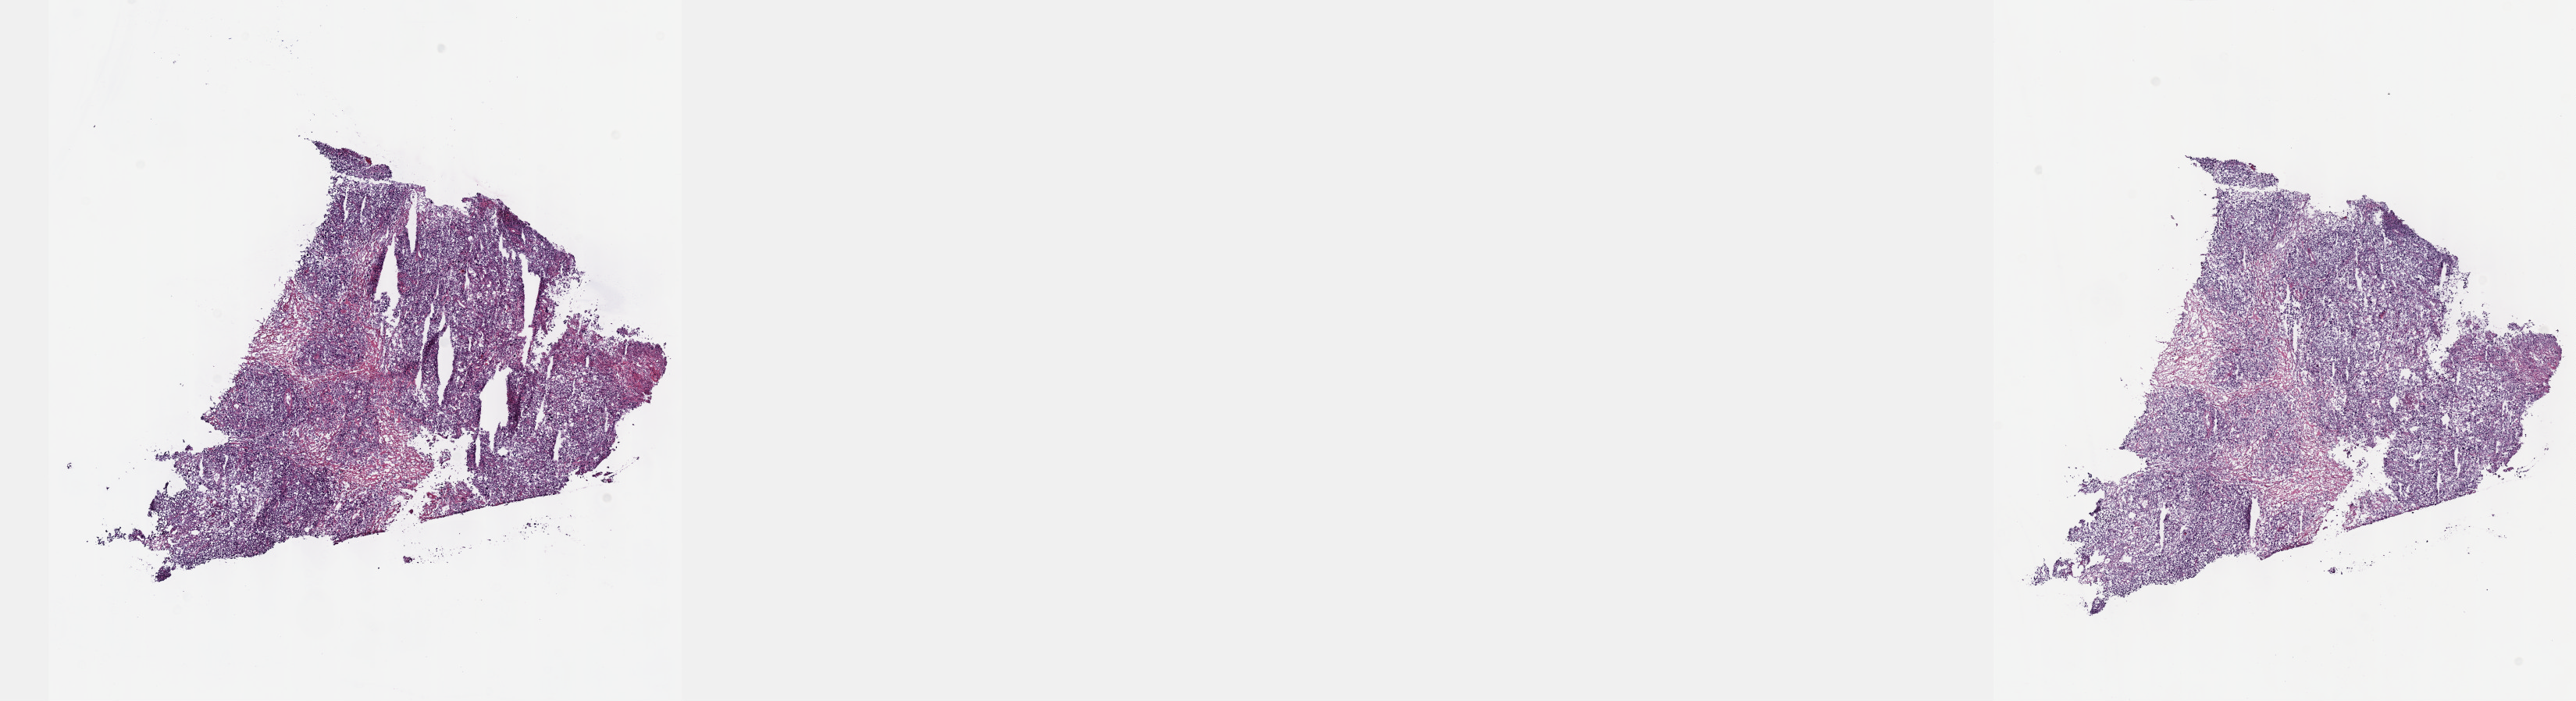
Whole-slide histology image, H&E, whole scanned area (about 26.7 x 7.3 mm) shown as a low-resolution overview, frozen section from the top of the tissue portion, cervix, primary tumour sample. Female, age 56 years at initial diagnosis. Histologic grade: G3 (poorly differentiated). Slide review estimates, as recorded: tumour cells 60%, tumour nuclei 60%, normal cells 15%, stromal cells 25%, necrosis 0%. Inflammatory infiltration, as recorded: lymphocyte infiltration 10%, monocyte infiltration 0%, neutrophil infiltration 2%.
* histologic diagnosis: Squamous cell carcinoma, large cell, nonkeratinizing, NOS
* FIGO stage: IB
* lymph nodes positive (case pathology): 0 of 29 examined